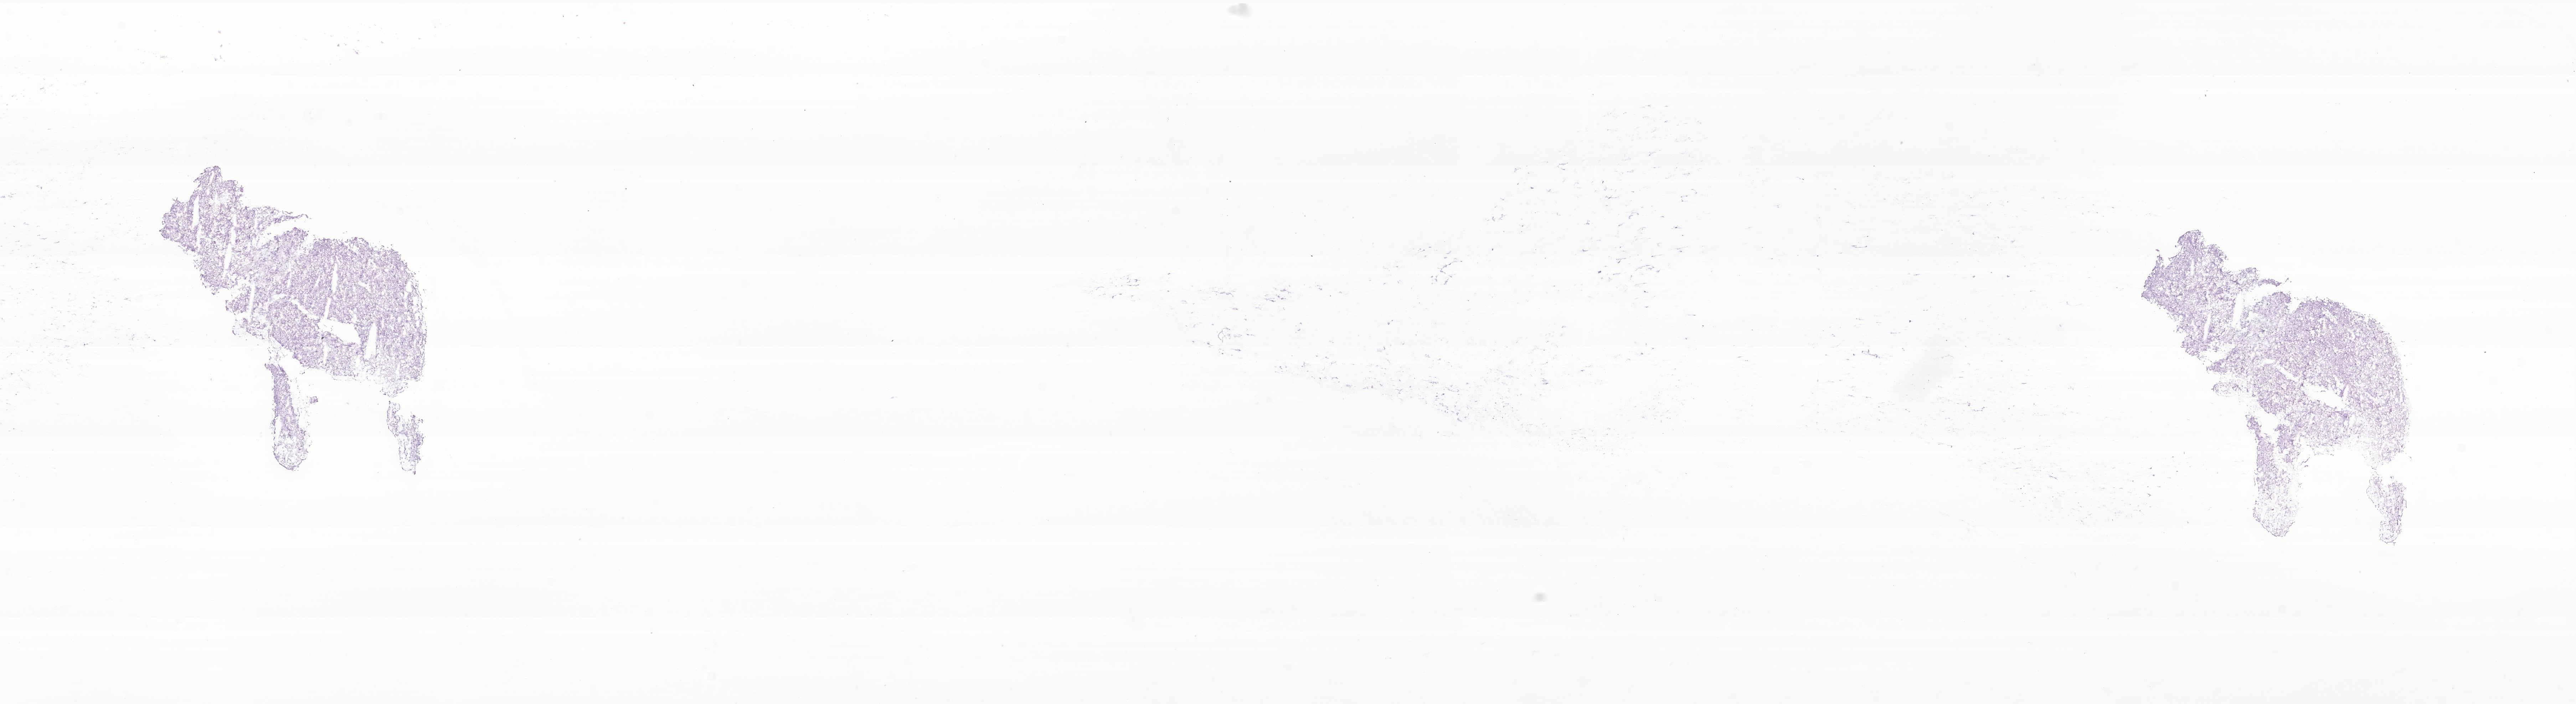
Whole-slide image, haematoxylin and eosin stain of tumor tissue from the brain, a low-resolution overview of the entire scanned area, about 30.5 x 8.3 mm. Cryosection (OCT / tissue freezing medium). Male patient, age 170 months (14 years 2 months).
Recorded diagnosis: Dysembryoplastic neuroepithelial tumor.